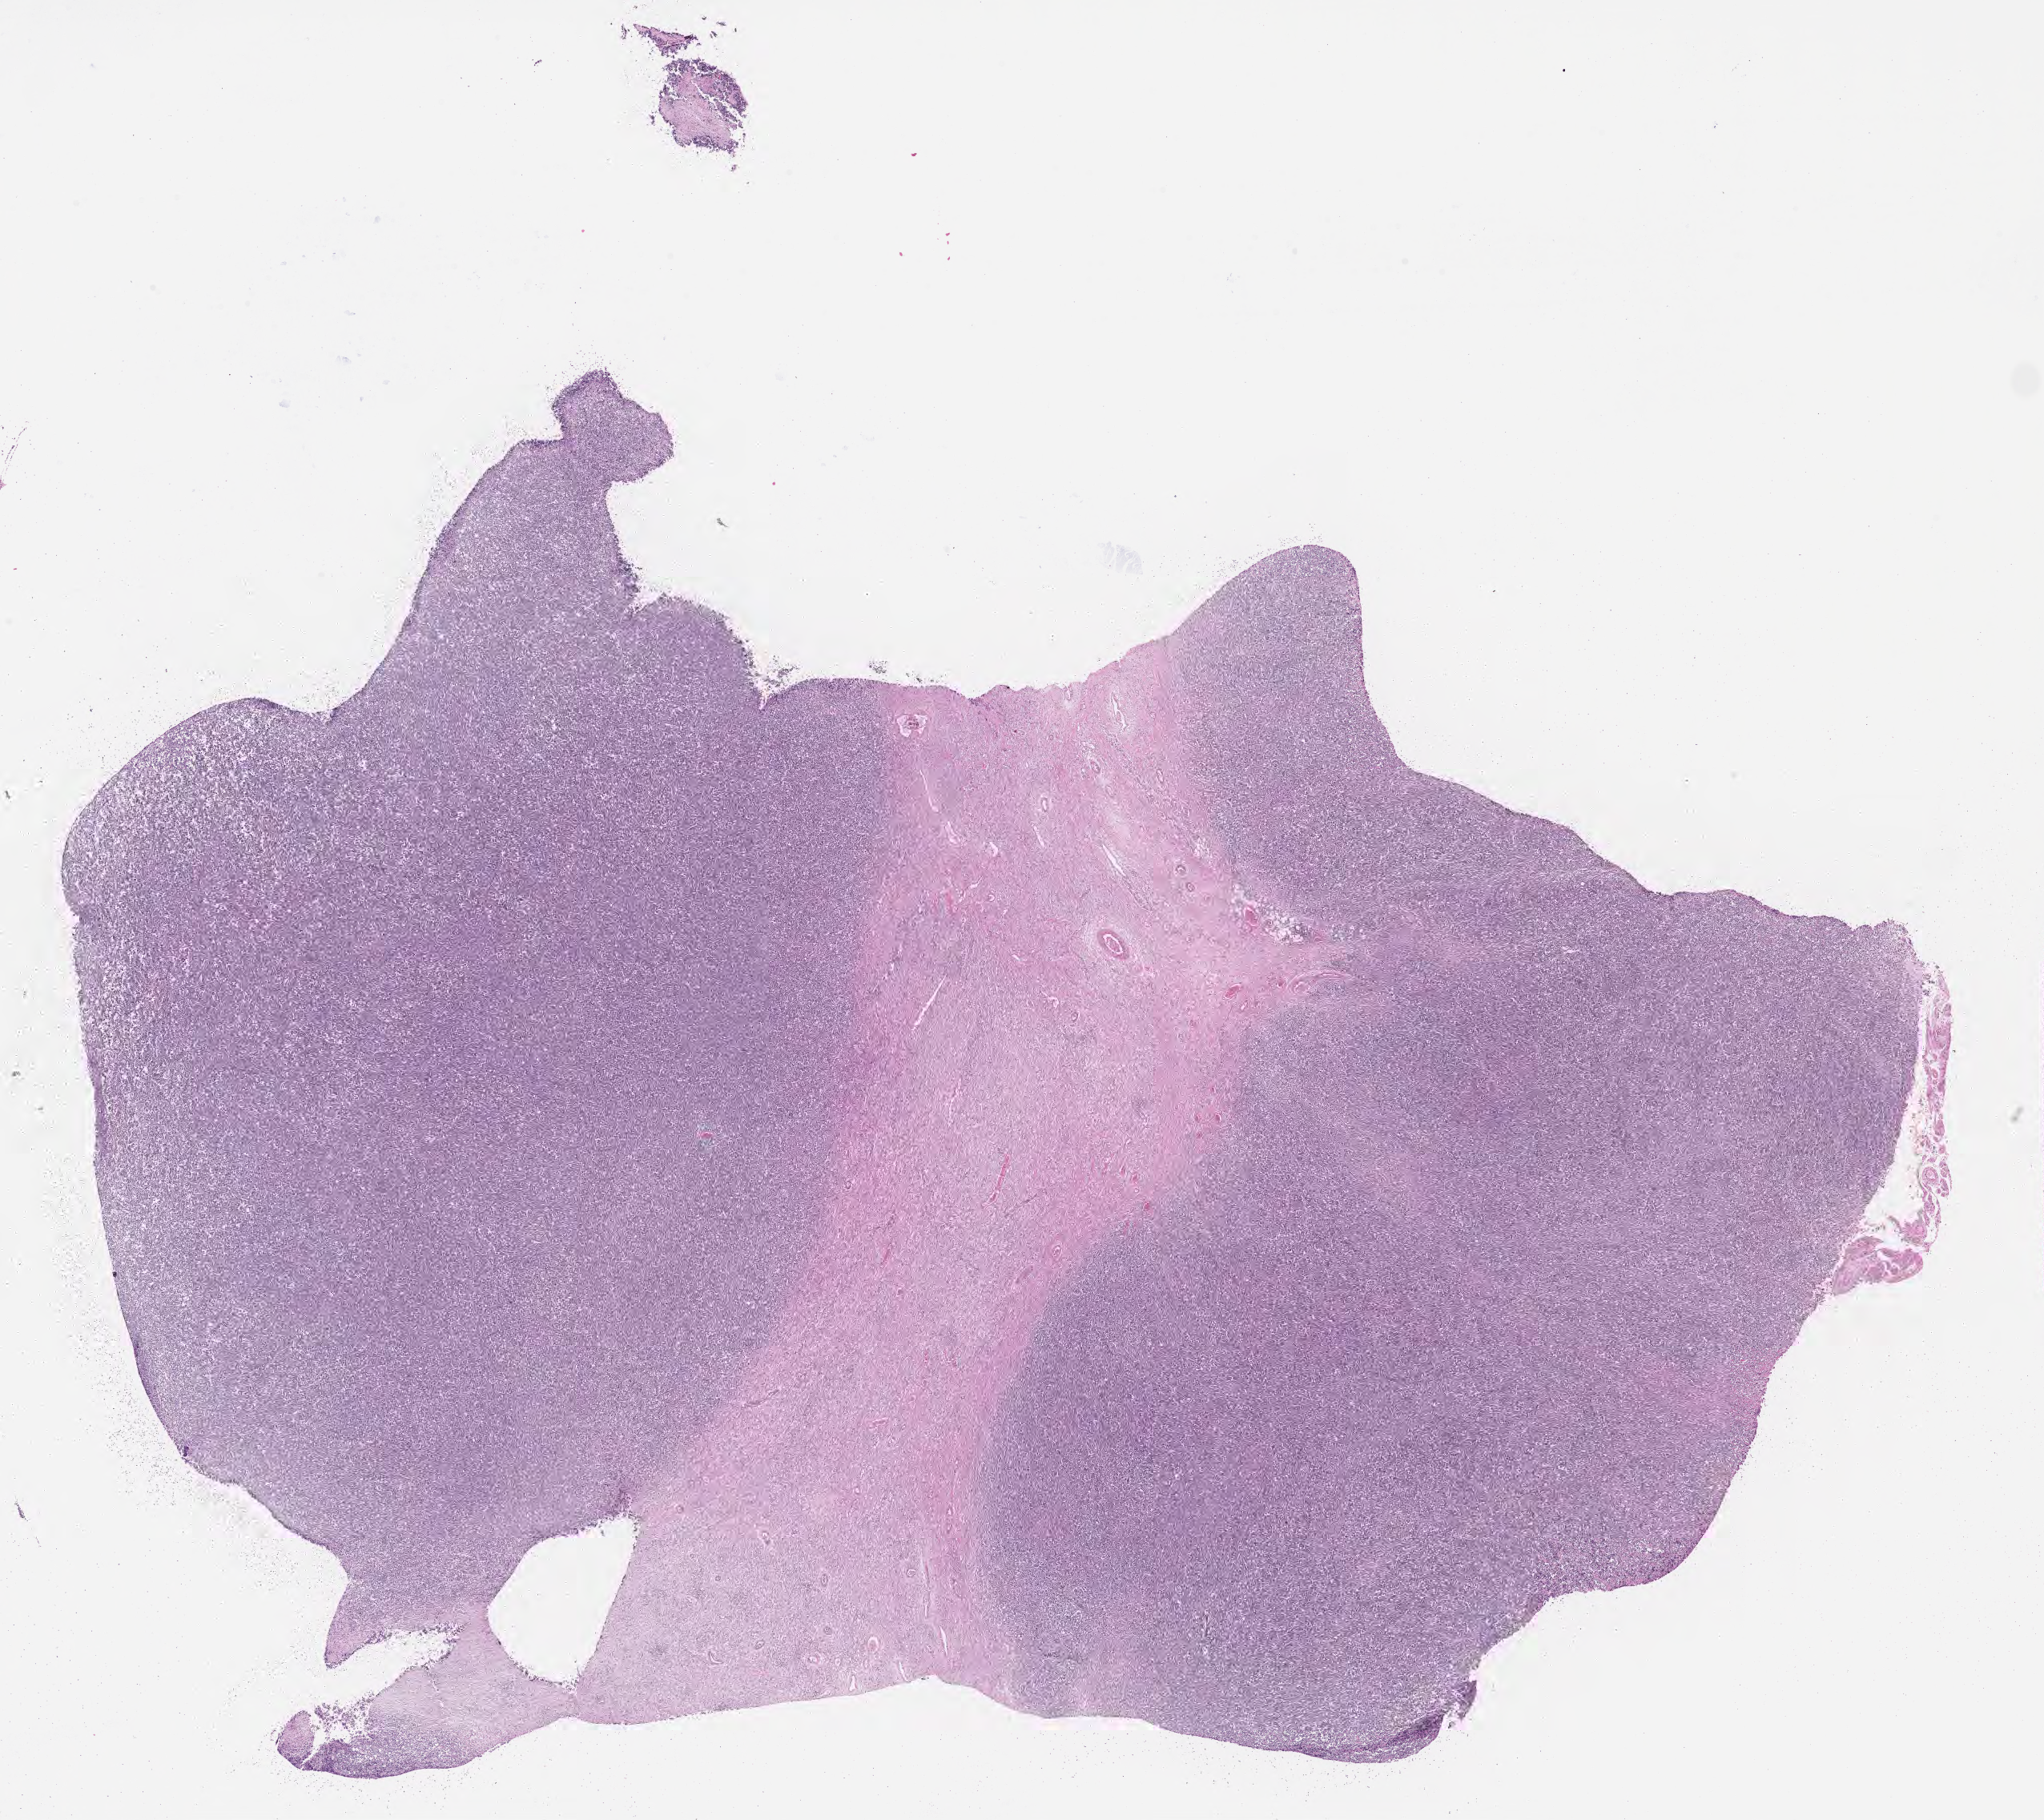
Digitized H&E-stained section, shown as a low-resolution overview of the whole scanned area (about 20.6 x 18.4 mm); formalin-fixed paraffin-embedded section; specimen: primary tumor. Female, age 8 years at initial diagnosis. Pathologist review of this section (percent, as recorded): tumor cells 75%, tumor nuclei 90%, stromal cells 20%, necrosis 5%, normal cells 0%. Infiltration values recorded for this section: lymphocyte infiltration 80%, monocyte infiltration 10%, neutrophil infiltration 0%.
Histologic diagnosis: Burkitt lymphoma, NOS. Ann Arbor stage (patient): Stage II.